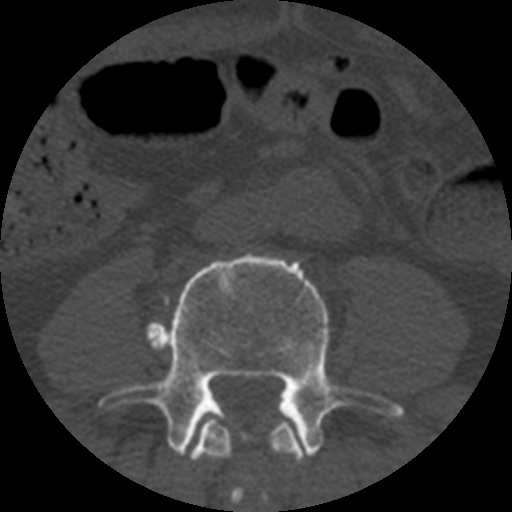
CT including the spine, one axial slice. Slice 98 of 508 in the series (ordered by position). Reconstruction kernel STANDARD. 120 kVp. Bone window (W 1800 / L 400 HU). 1.25 mm slice thickness. 512 × 512 image matrix, field of view 160 × 160 mm. Patient age 57 years. From the clinical record (not read from this slice): primary cancer: prostate.
Structures marked on this image (semi-automatic segmentation, software-assisted and operator-edited):
- L3 vertebra: box from (x=190, y=415) to (x=305, y=505) px
- L4 vertebra: (x=99, y=253)–(x=404, y=457)